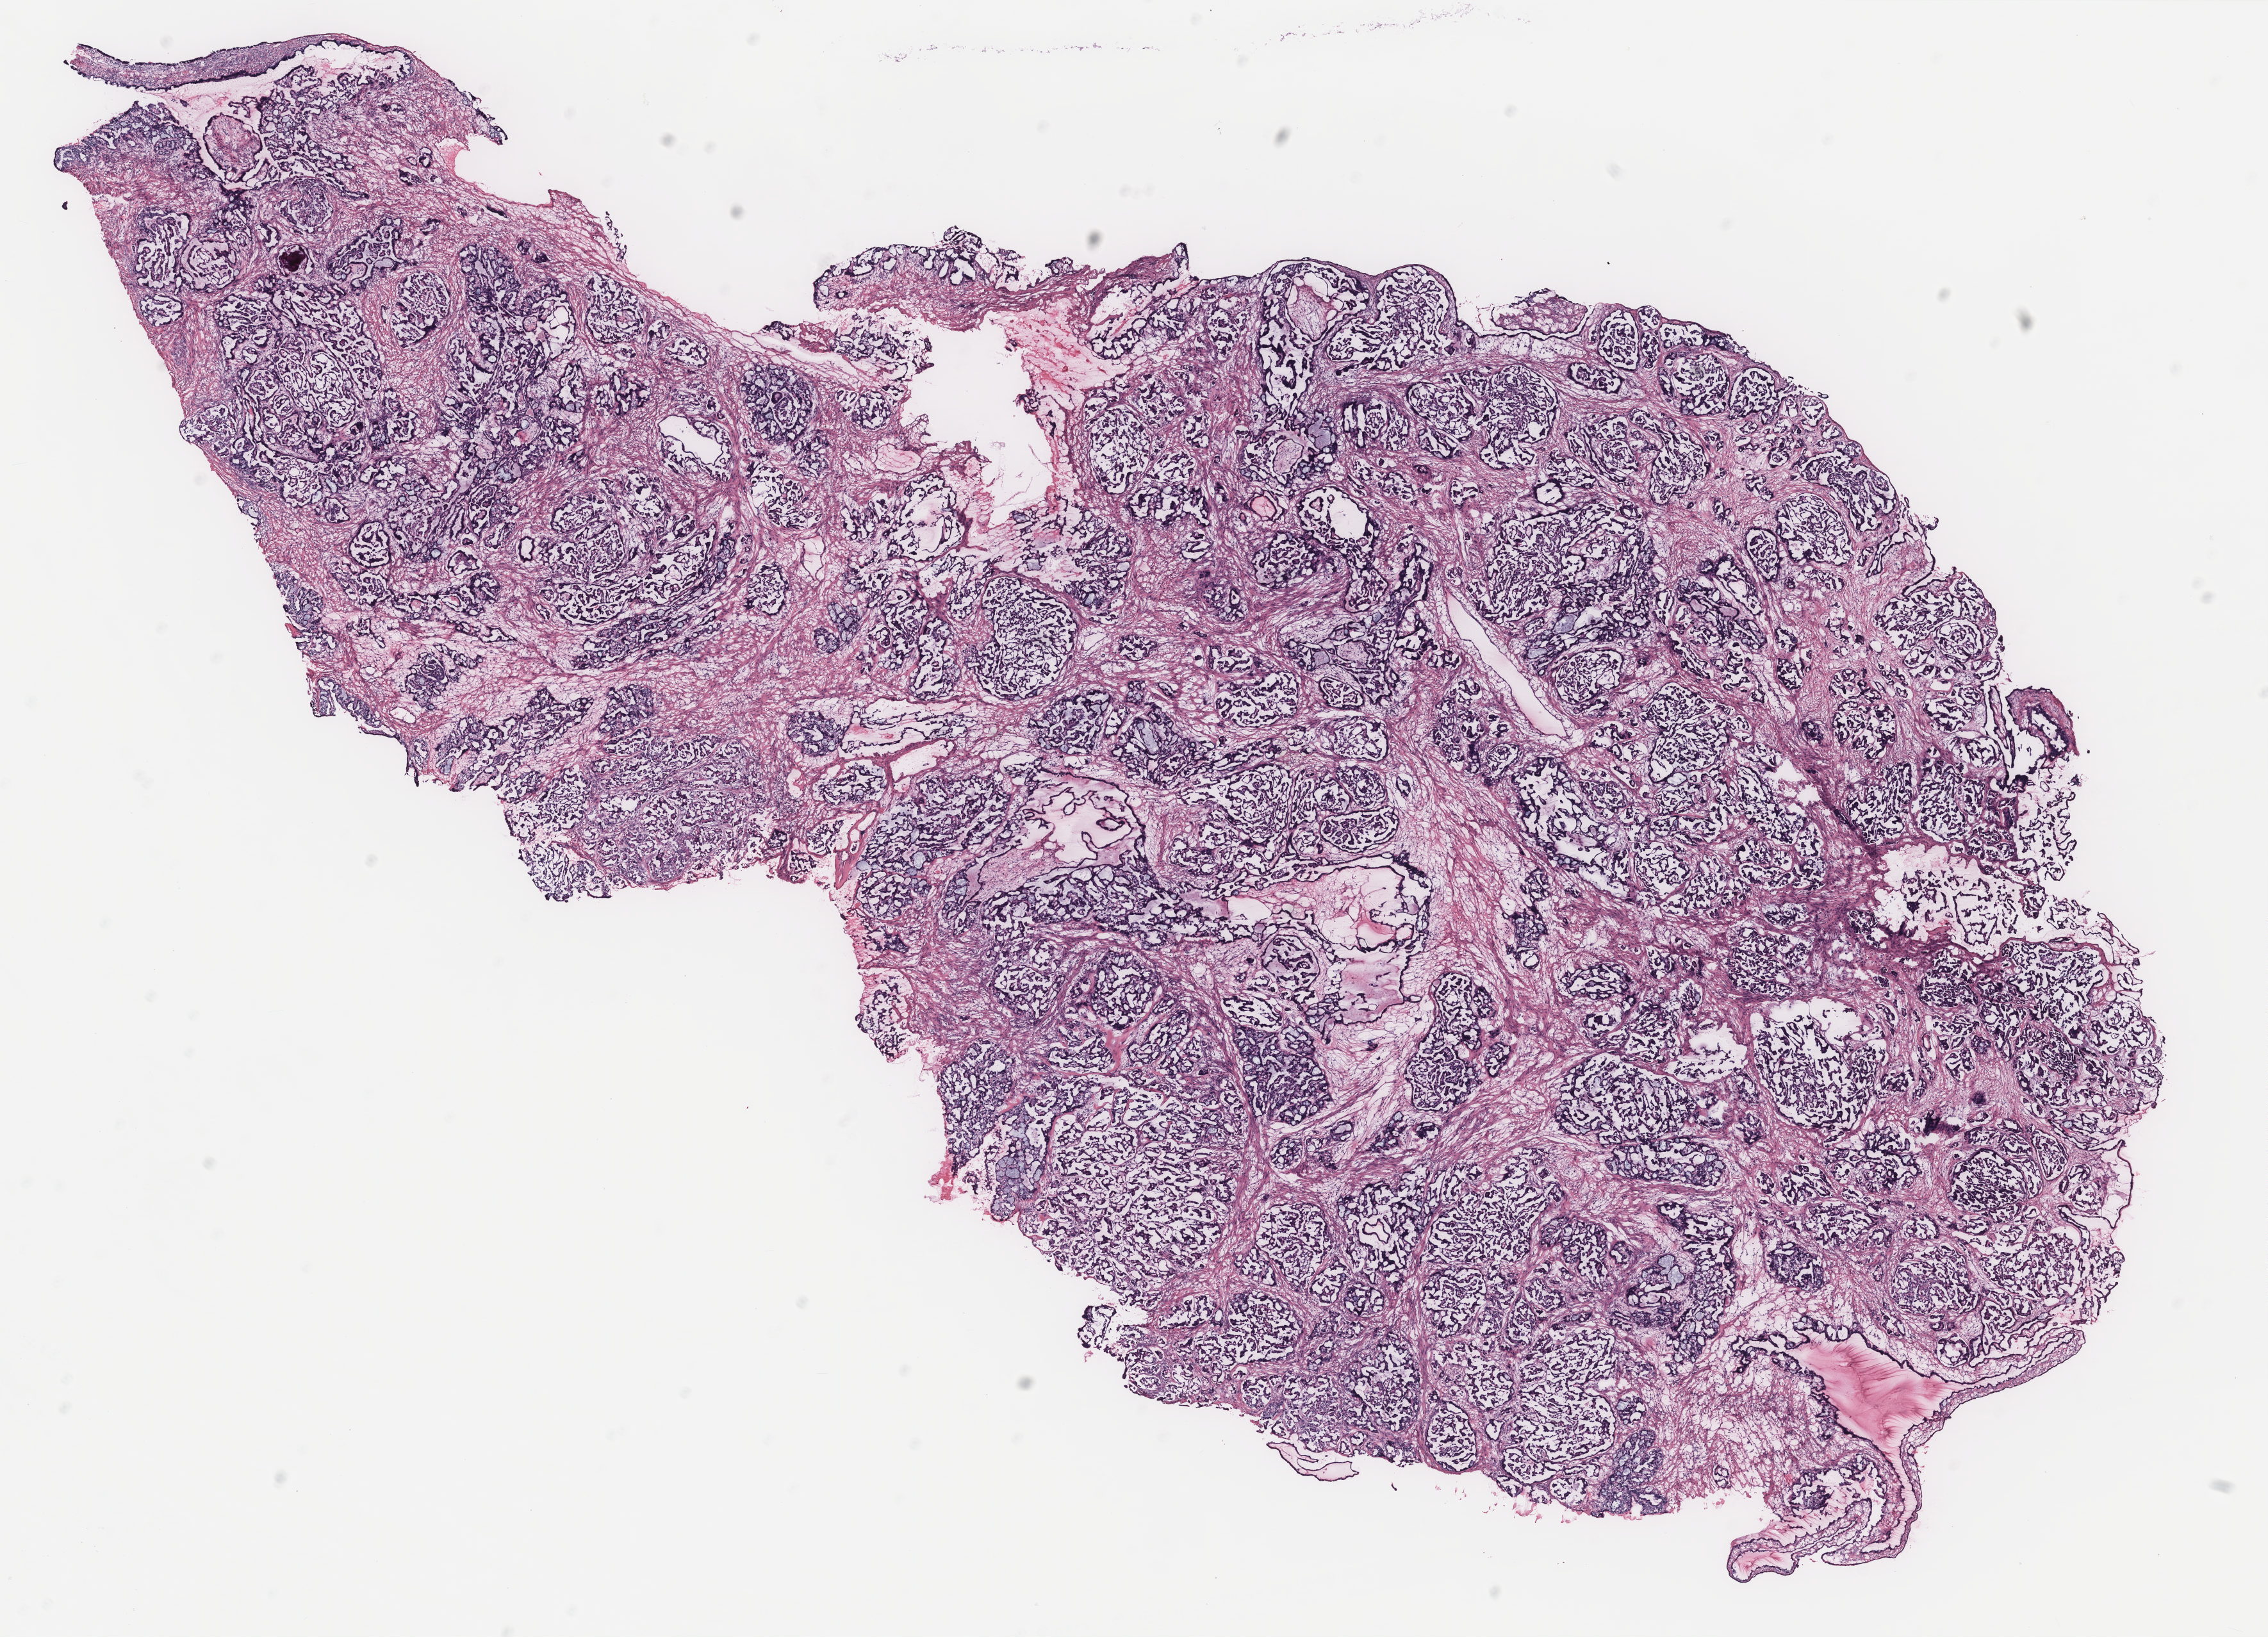
Whole-slide histology image, Hematoxylin and eosin (H&E) stained — a low-resolution overview of the entire scanned area, about 14.2 x 10.2 mm; tumour tissue sample, ovary. Female, 73 y/o.
Diagnosis: Serous adenocarcinoma, NOS. Primary tumour site (as recorded): ovary.